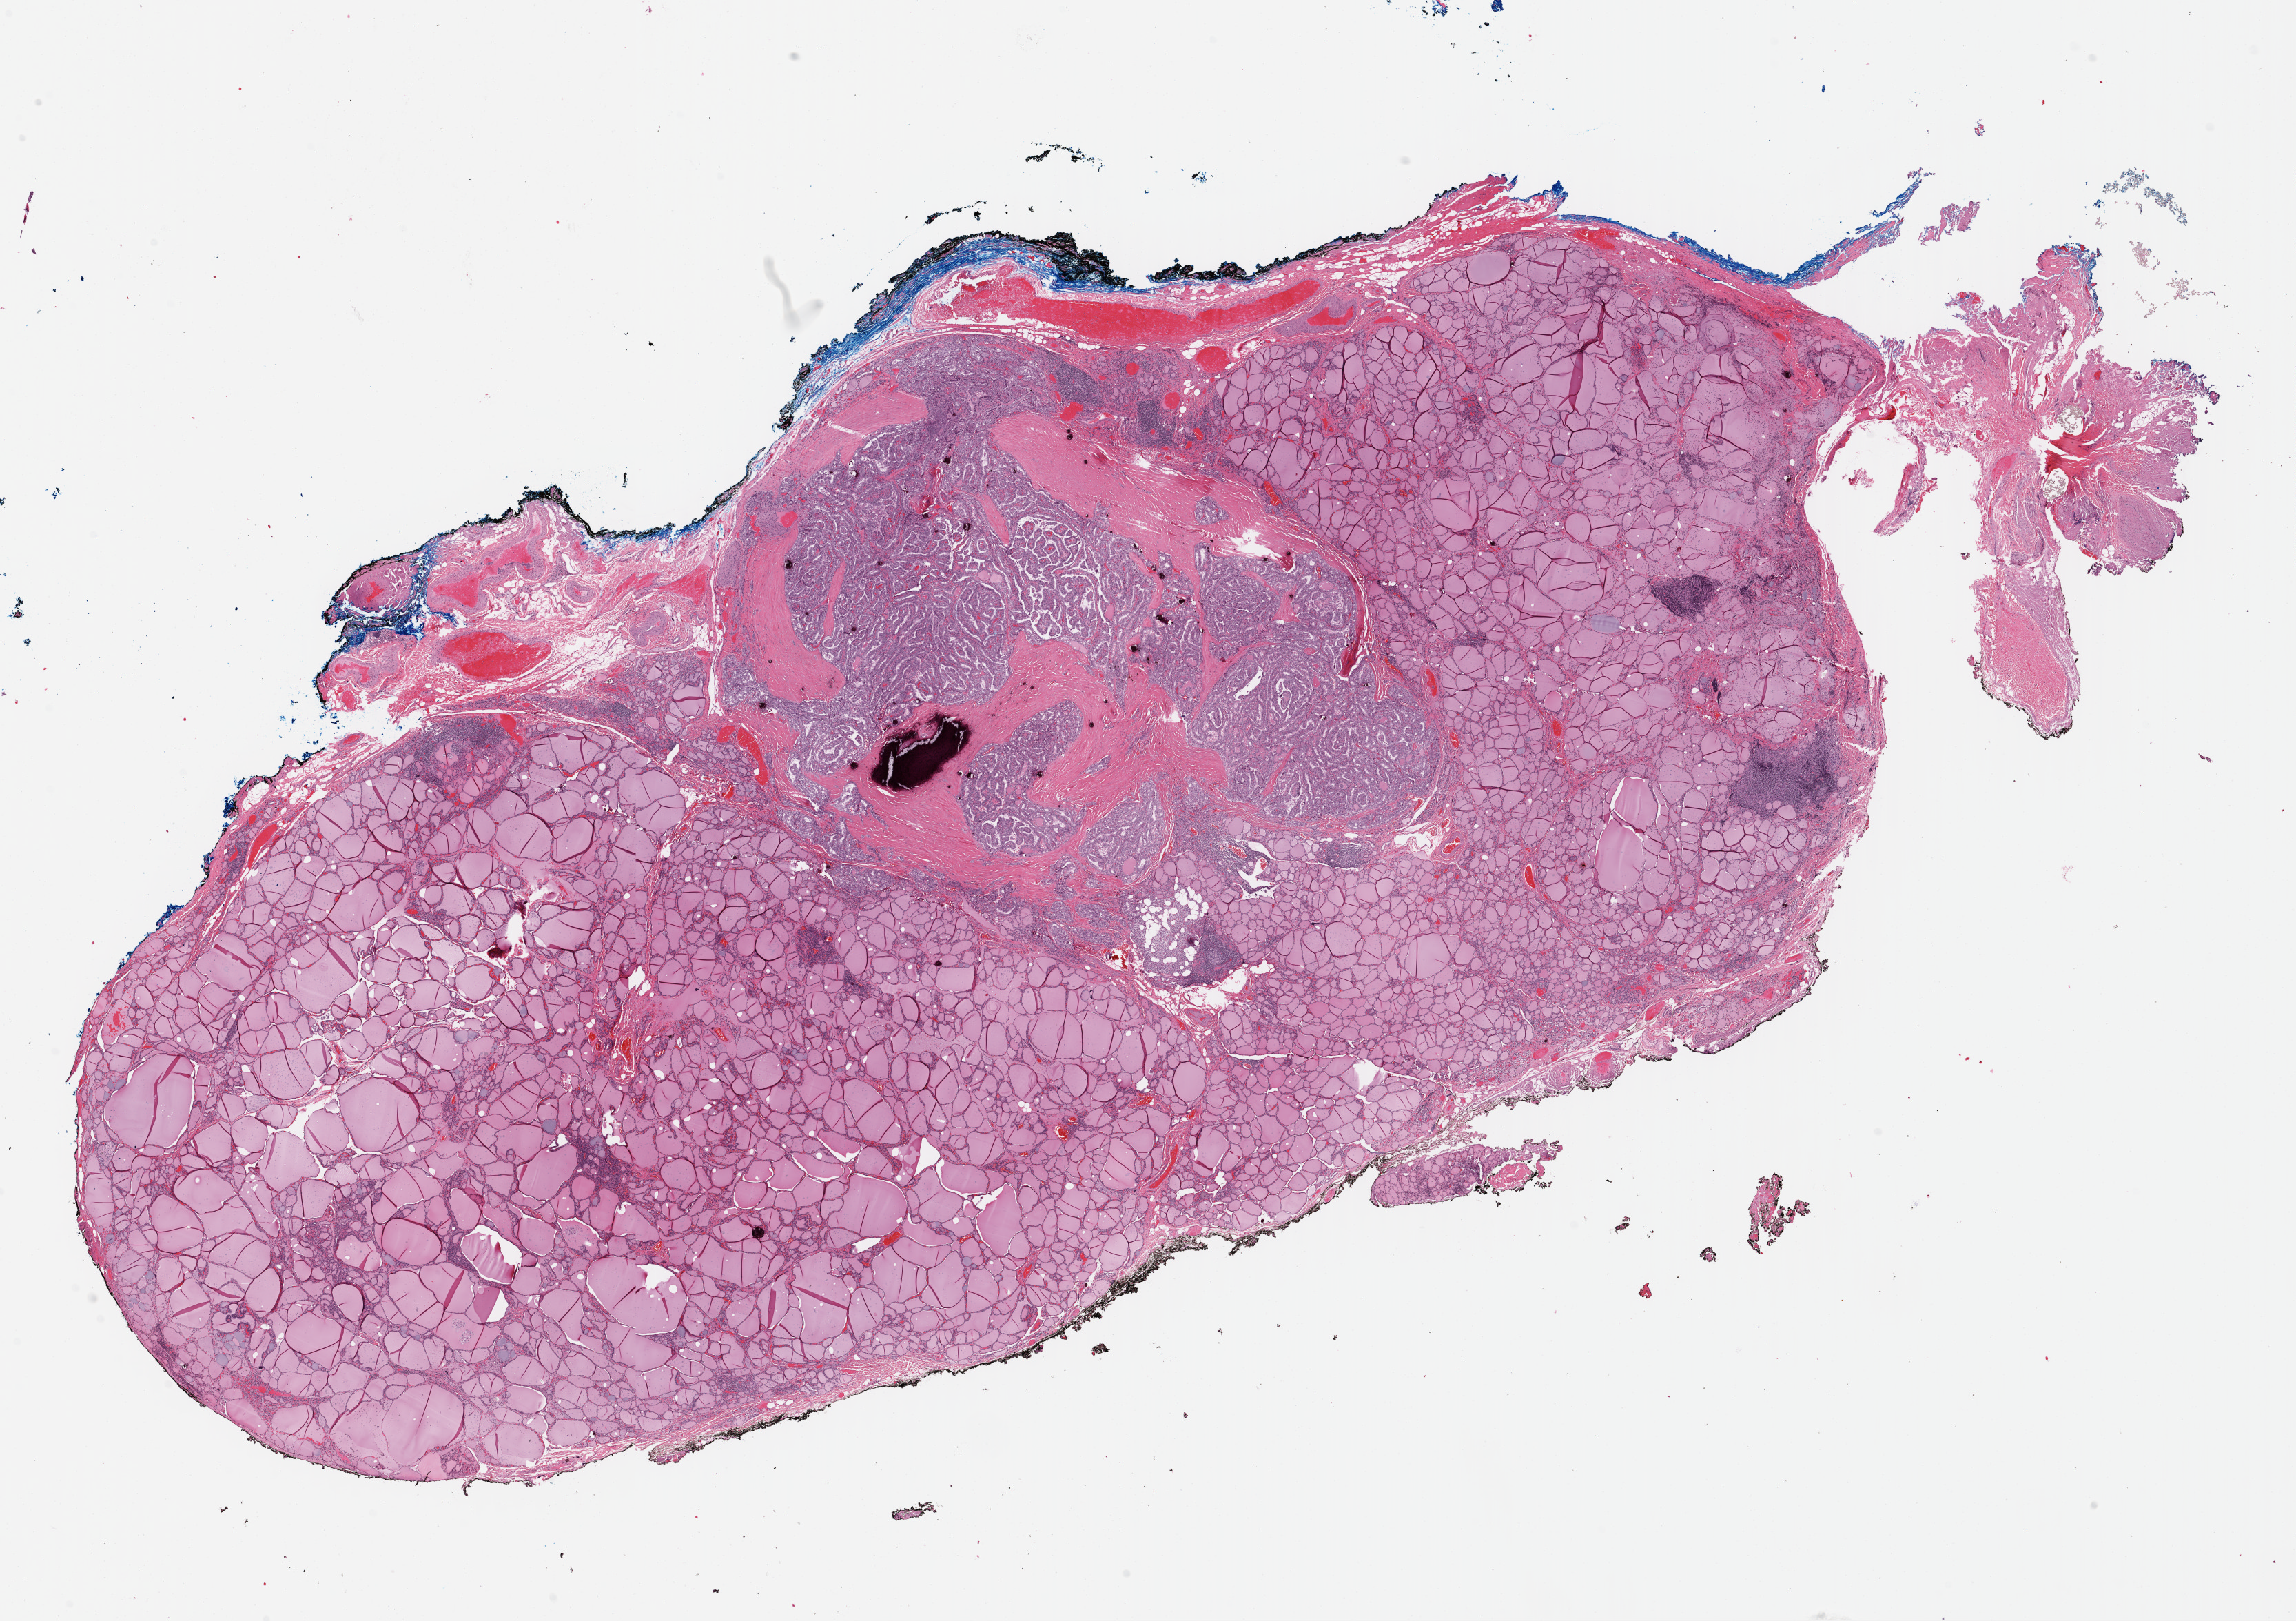
Hematoxylin and eosin (H&E) stained whole-slide image, whole scanned area (about 26.2 x 18.5 mm, acquisition: 40x scan) shown as a low-resolution overview, formalin-fixed paraffin-embedded (FFPE) diagnostic section, thyroid, primary tumour sample. Female, age 40 years at initial diagnosis.
Diagnosis: Papillary adenocarcinoma, NOS (thyroid gland).